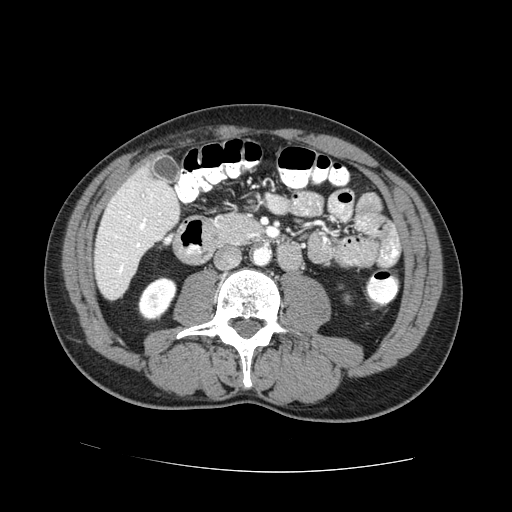
Contrast-enhanced abdominal CT (liver protocol), one axial slice. Reconstruction kernel STANDARD. One of 2 acquisitions stored at this slice position. Soft-tissue window (W 400 / L 40 HU). 2.5 mm slice thickness. 512 × 512 image matrix, field of view 380 × 380 mm. From the clinical record (not read from this slice): diagnosis: hepatocellular carcinoma (patient treated with transarterial chemoembolisation; whether this scan precedes or follows treatment is not stated here); TNM stage (as recorded): Stage-IVA.
Annotated regions visible in this slice (semi-automatic segmentation, software-assisted and operator-edited):
- liver parenchyma outside the tumour (the mass and vessels are separate outlines, so this box may not span the whole liver): bounding box (x1, y1, x2, y2) in pixels: (94, 157, 180, 300)
- liver vessels: (115, 194, 153, 273)